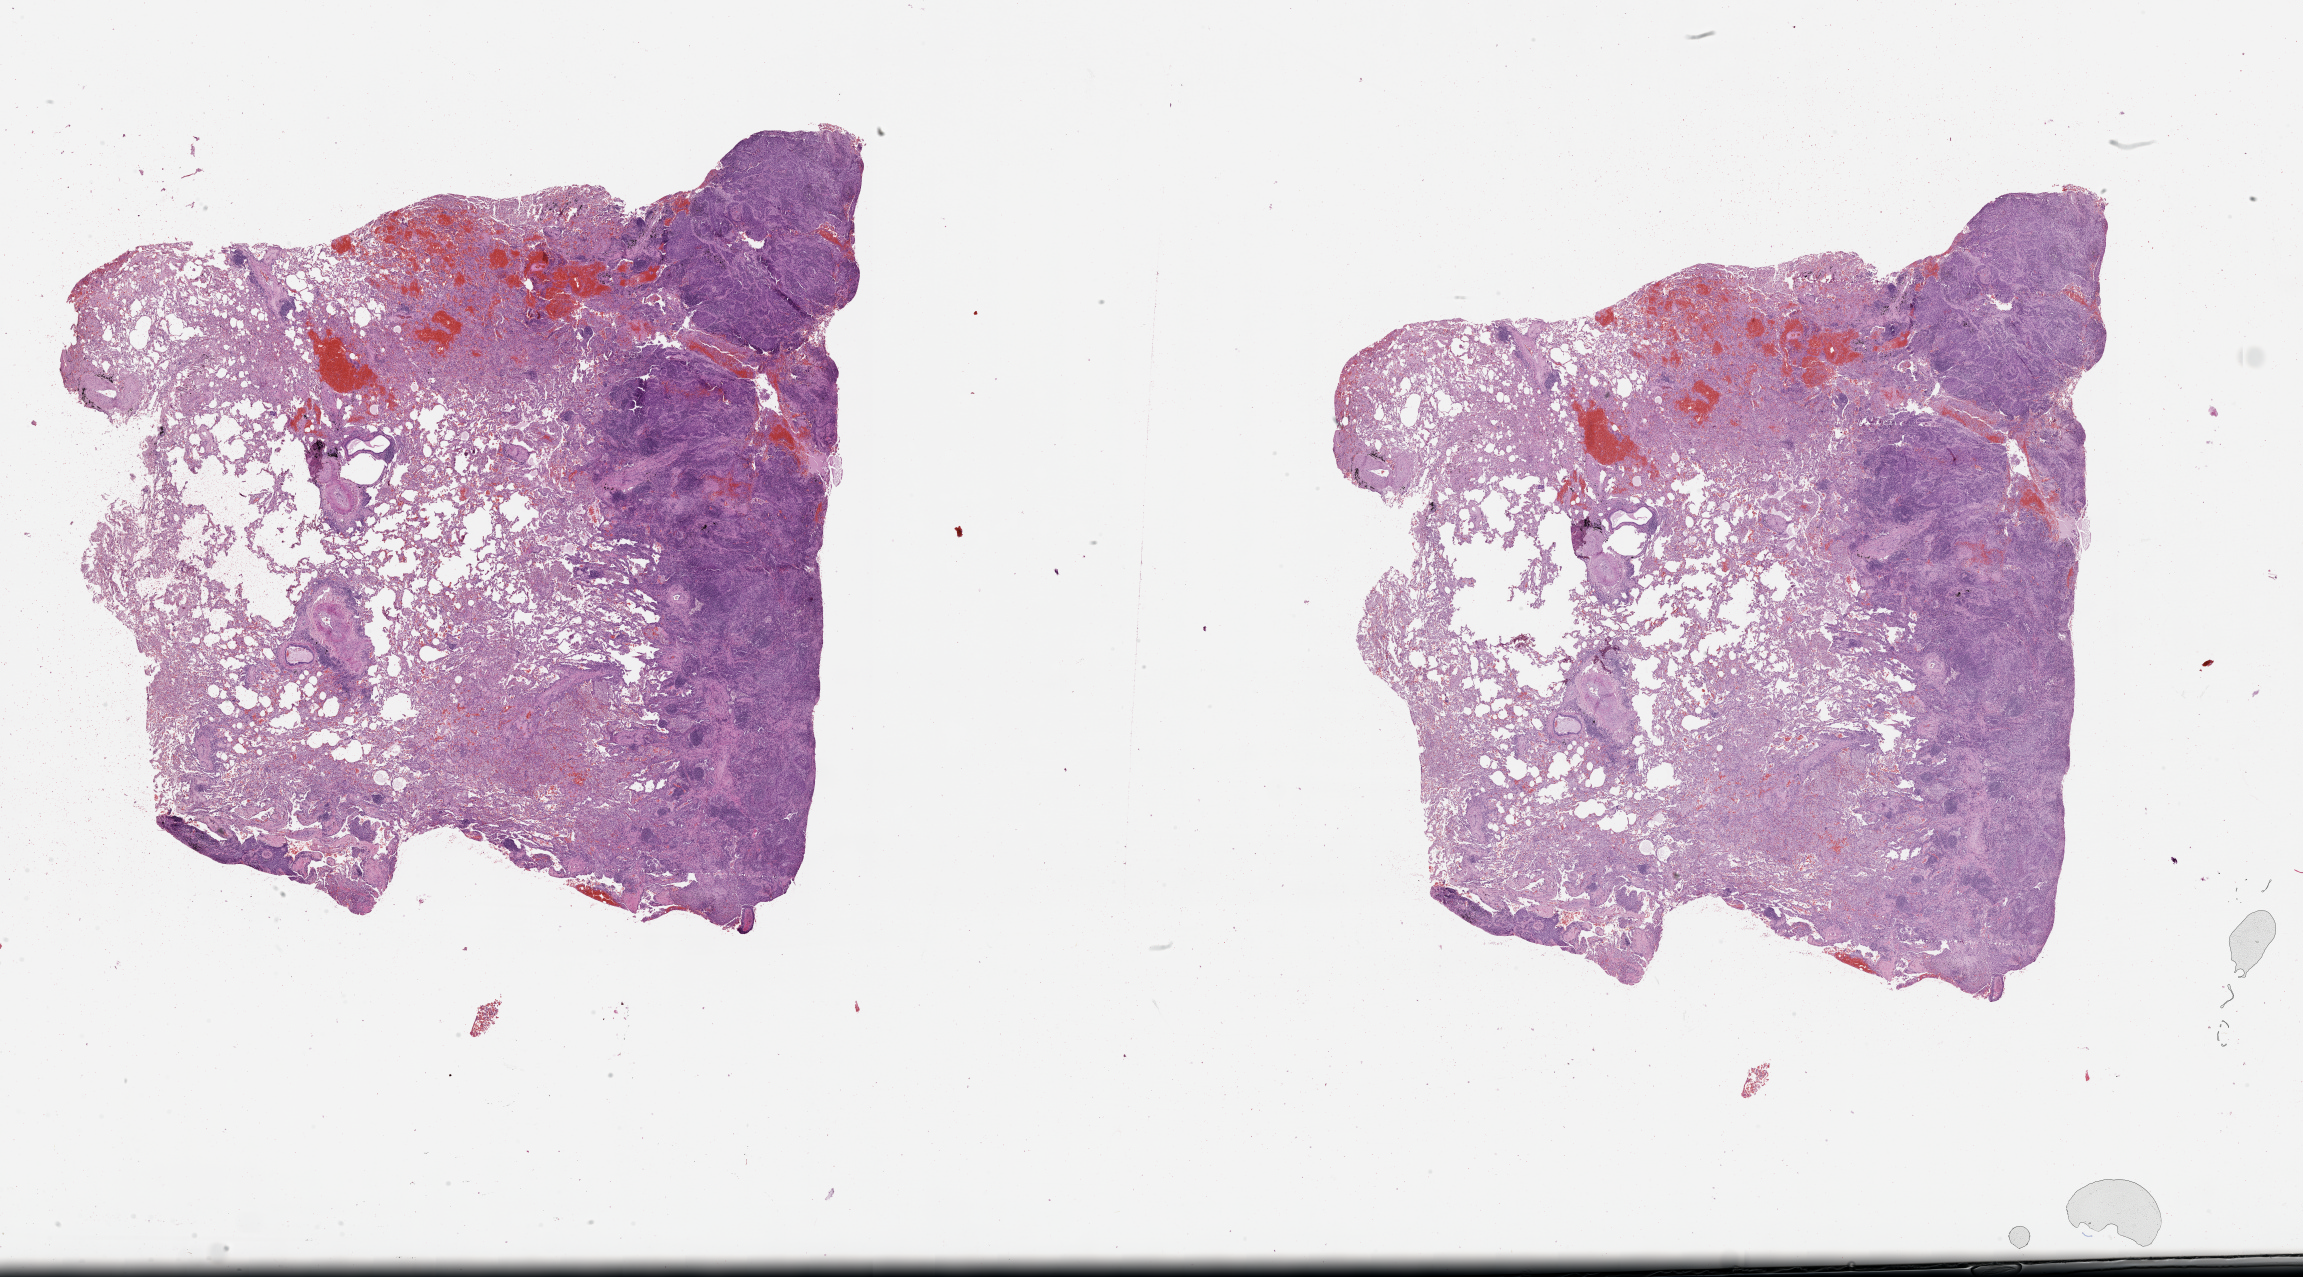
Whole-slide histology image, H&E — low-resolution overview of the scanned area, about 37.1 x 20.6 mm. Lung, tumour tissue. 74-year-old male patient.
Patient diagnosis (cohort enrolment): squamous cell carcinoma (lung).